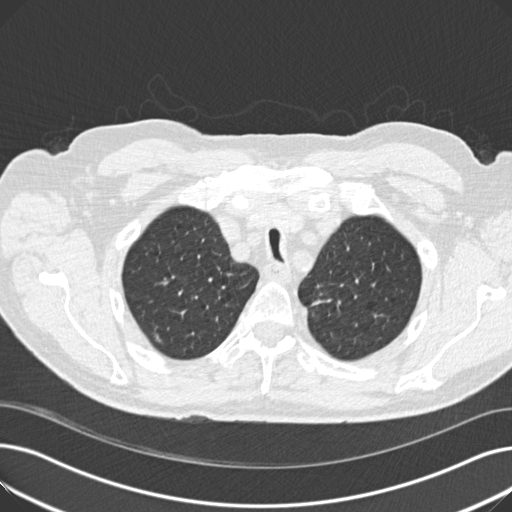
Low-dose screening chest CT, one axial slice. Lung window (W 1500 / L -600 HU). 2 mm slice thickness. 512 × 512 image matrix, field of view 370 × 370 mm.
Annotated regions visible in this slice (outlined manually by an expert reader):
- lesion 1 (tumor, upper lobe of left lung): bounding box [x1, y1, x2, y2] px = [312, 300, 322, 305]